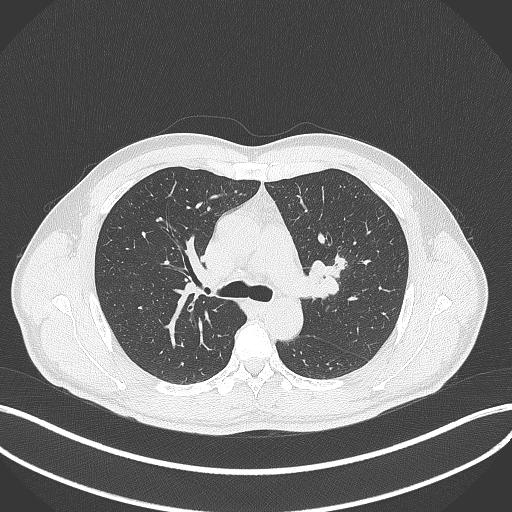
Chest CT, one axial slice; slice 276 of 392 in the series (ordered by position); reconstruction kernel B70f; 120 kVp; lung window (W 1500 / L -600 HU); 512 × 512 image matrix. Patient: male, 50 years. From the clinical record (not read from this slice): clinical TNM (as recorded): T1c N1 M1b.
Outlined on this slice (bounding box drawn by a radiologist):
- lung tumour (recorded histology: squamous cell carcinoma): bounding box (x1, y1, x2, y2) in pixels: (305, 251, 348, 283)